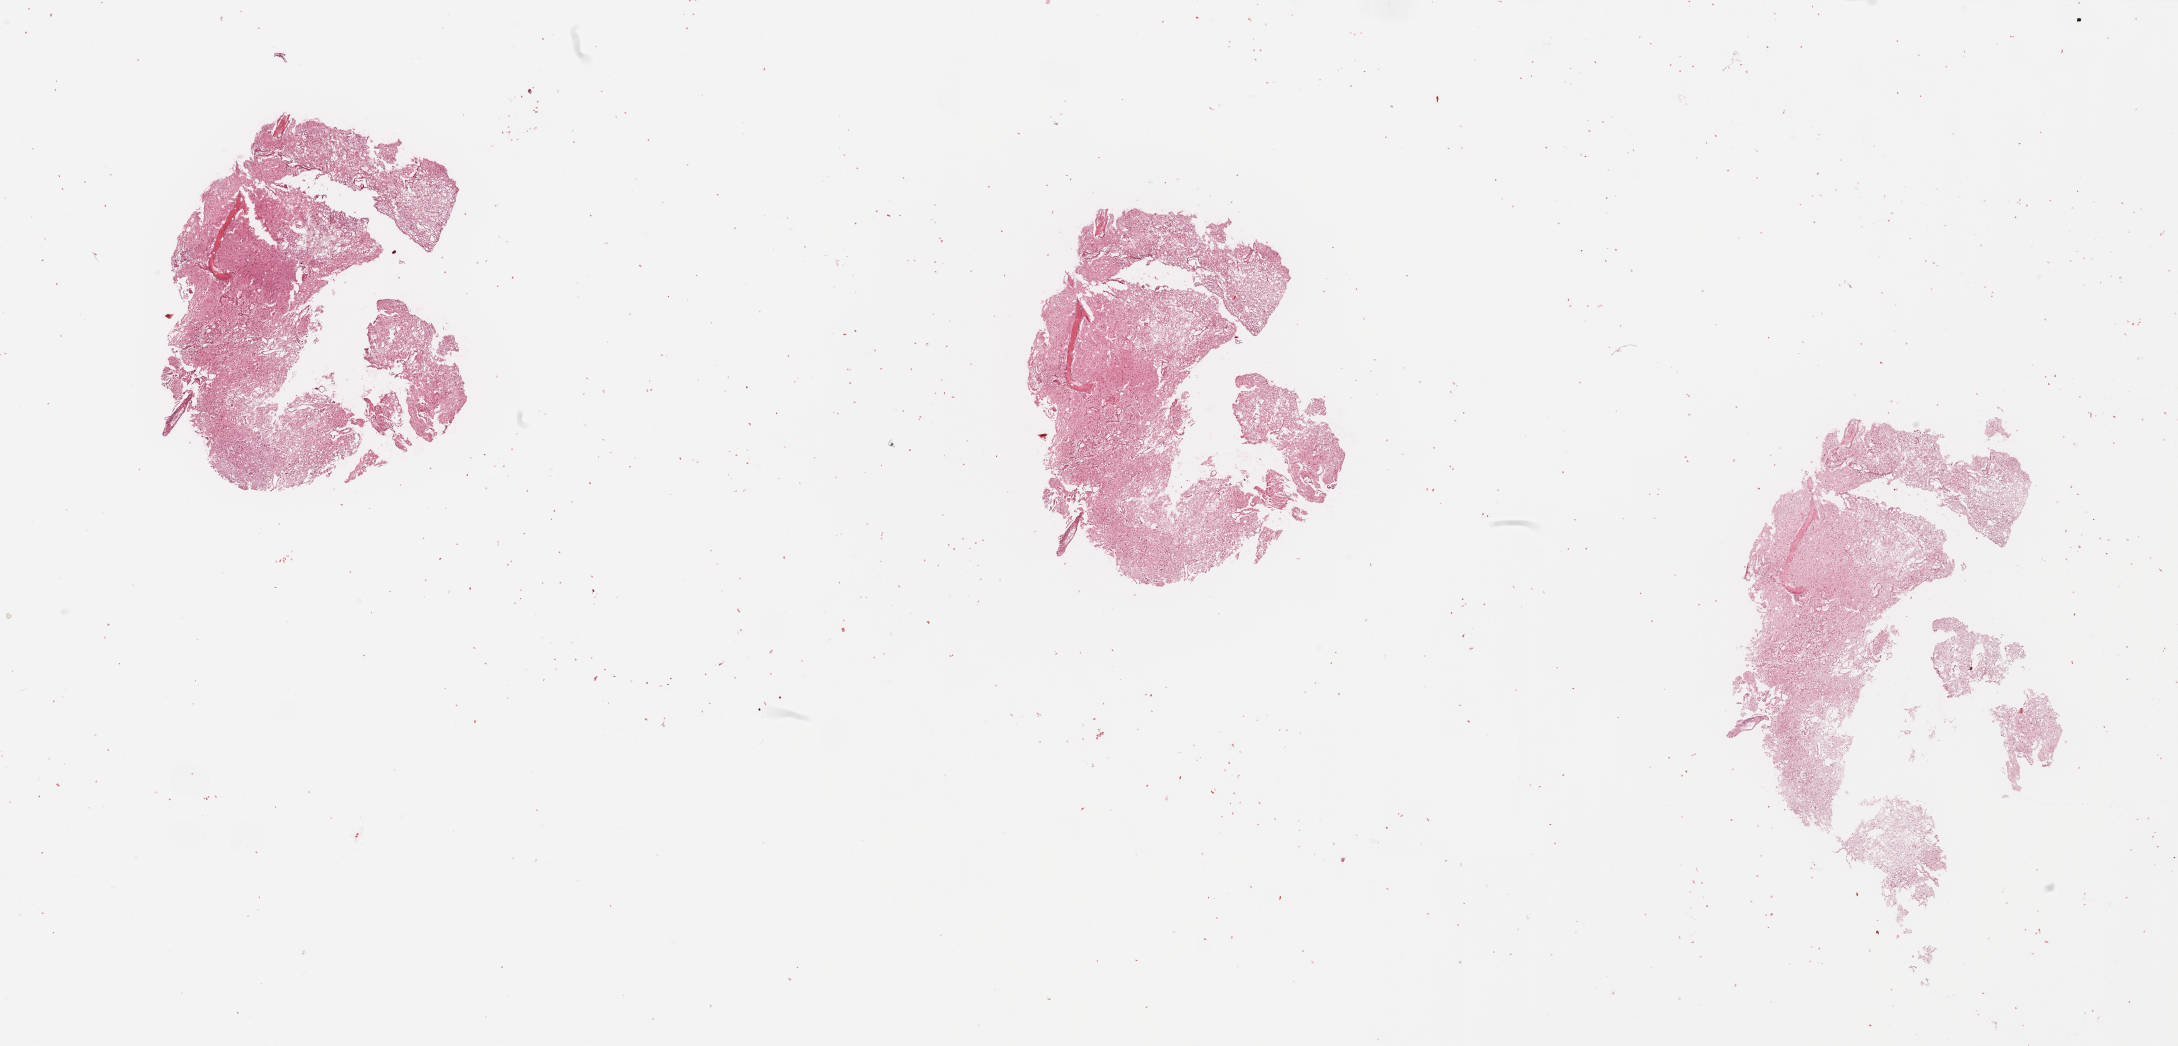
H&E whole-slide image, whole scanned area (about 34.5 x 16.5 mm, slide scanned at 20x) shown as a low-resolution overview, tumour tissue sample, sampled site: brain. Female, 57 y/o. Composition of this section per pathologist review: tumour nuclei 90%, necrosis 5%.
Diagnosis: Glioblastoma. Primary tumour site (as recorded): temporal lobe.